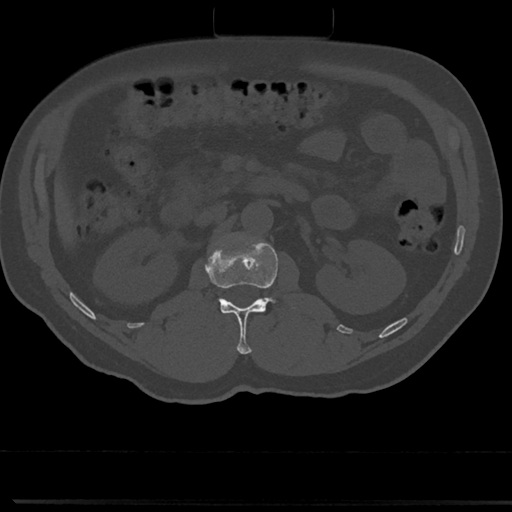
CT including the spine, one axial slice; slice 68 of 817 in the series (ordered by position); bone window (W 1800 / L 400 HU); 0.5 mm slice thickness; 512 × 512 image matrix, field of view 355 × 355 mm. Male patient, age 61 years. Case-level facts recorded for this patient, not image findings: primary cancer: prostate.
Structures marked on this image (semi-automatic segmentation, software-assisted and operator-edited):
- L1 vertebra: bounding box (x1, y1, x2, y2) in pixels: (206, 235, 301, 354)